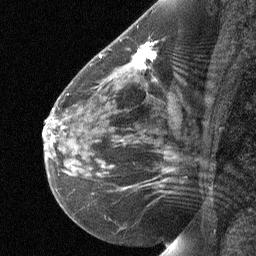
Breast MRI (dynamic contrast-enhanced), one sagittal slice; slice 35 of 64 in the series (ordered by position); dynamic contrast-enhanced study with each time point stored as its own series, time point 2 of 3 at this slice position (early post-contrast, ordered by acquisition time); 1.5 T; TE 4.8 ms, TR 27 ms; 256 × 256 image matrix, field of view 180 × 180 mm. Patient: female, 51 years. From the clinical record (not read from this slice): setting: breast cancer imaged before/during neoadjuvant chemotherapy; receptor status: HR-positive, HER2-negative.
Annotated regions visible in this slice (semi-automatic segmentation, software-assisted and operator-edited):
- analysis volume of interest (the breast-tissue region the enhancement analysis was run in; not a lesion): bounding box (x1, y1, x2, y2) in pixels: (81, 35, 179, 103)
- tumour enhancement mask (voxels above the 90 % enhancement threshold inside the analysis volume of interest): (133, 43, 156, 67)